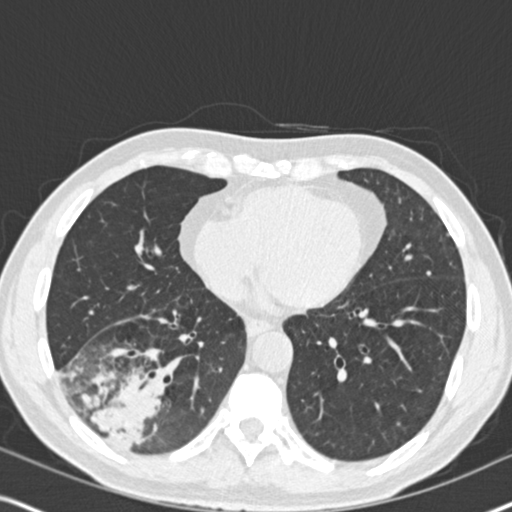
Low-dose screening chest CT, one axial slice; position 76 of 182 along the scan axis; reconstruction kernel B30f; lung window (W 1500 / L -600 HU); 2 mm slice thickness; 512 × 512 image matrix.
Annotated regions visible in this slice (outlined manually by an expert reader):
- lesion 1 (tumor, lower lobe of right lung): bounding box (x1, y1, x2, y2) in pixels: (88, 375, 160, 449)